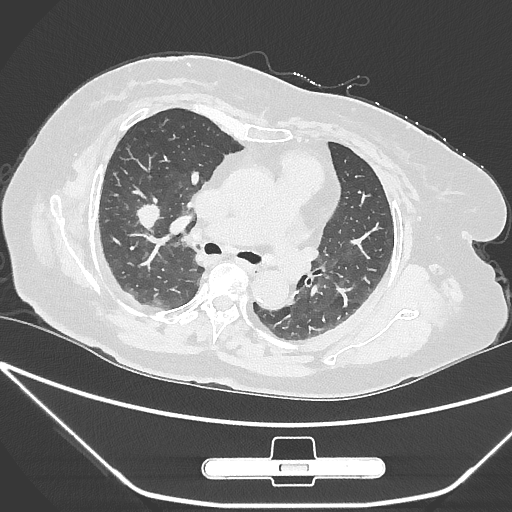
Chest CT, one axial slice; position 162 of 245 along the scan axis; lung window (W 1500 / L -600 HU); 512 × 512 image matrix. Female patient, age 65 years. Case-level facts recorded for this patient, not image findings: clinical TNM (as recorded): T1c N0 M0.
Outlined on this slice (rectangle marked by the reading radiologist):
- lung tumour (recorded histology: adenocarcinoma): box from (x=128, y=195) to (x=170, y=227) px